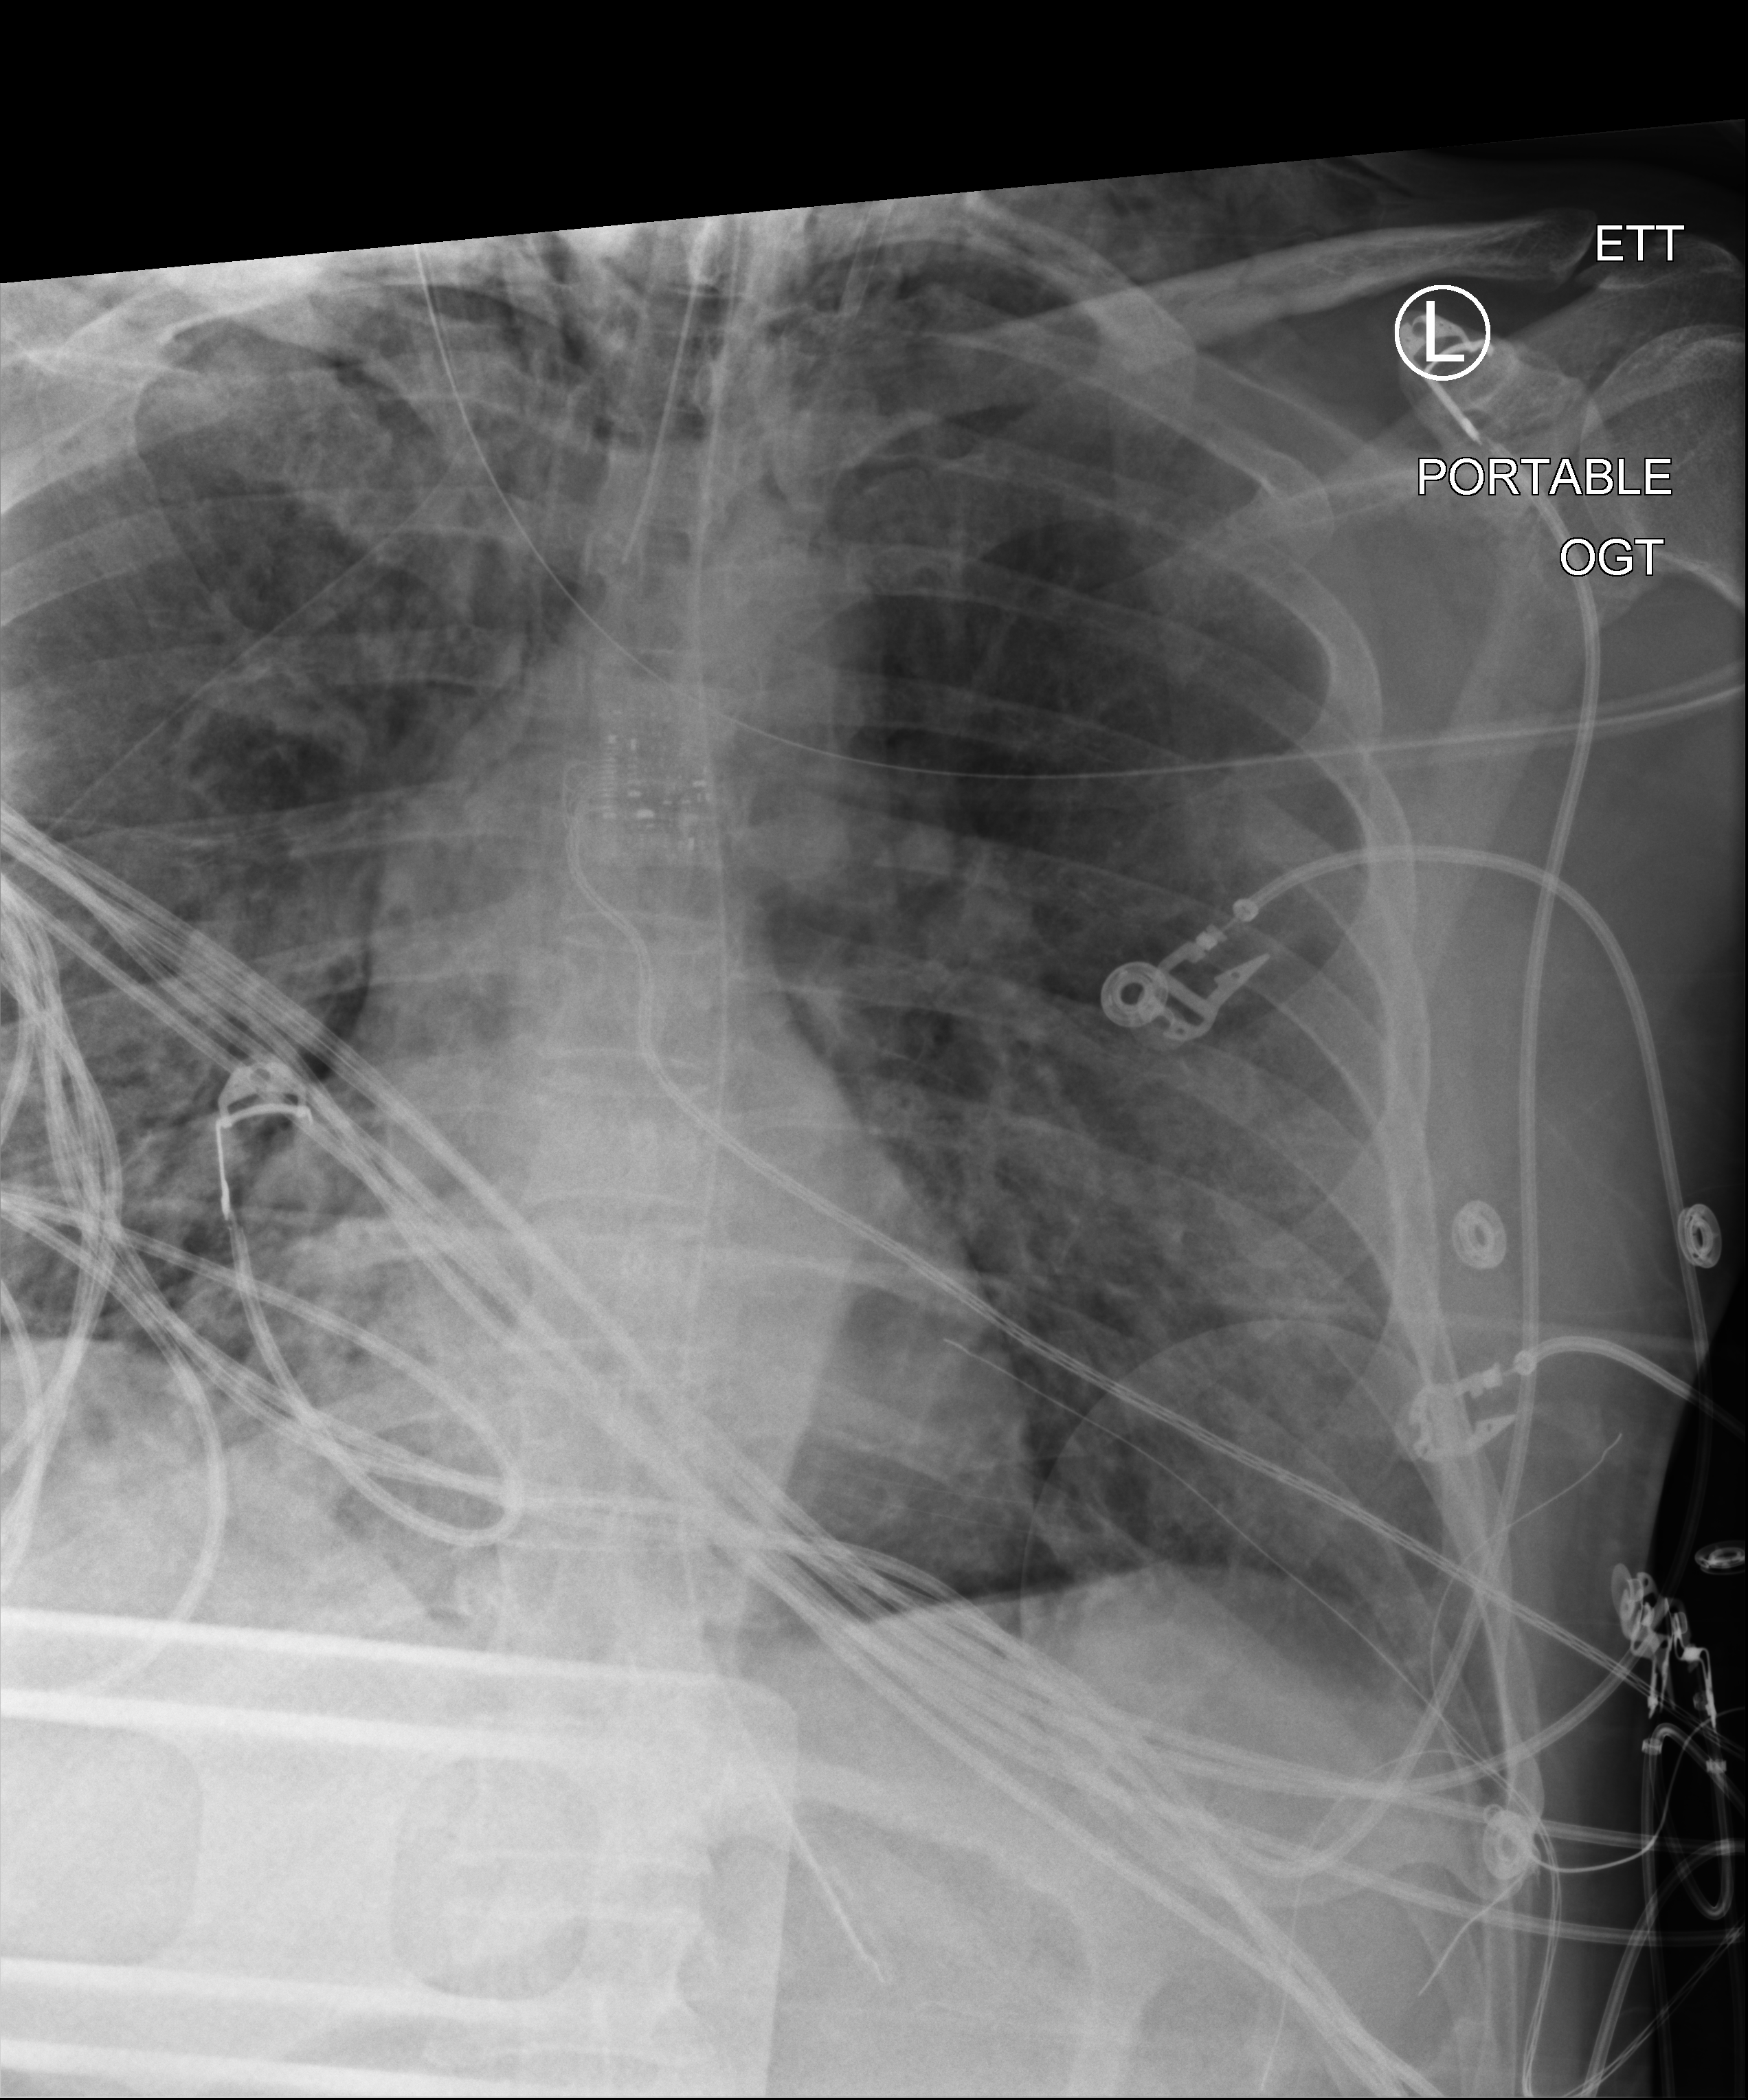
Chest X-ray (portable), anteroposterior (AP) projection. Male patient hospitalised with COVID-19, age 60–74 years.
Admission-level facts for this patient (not findings on this image; timing relative to this image not recorded):
- COPD (admission record): no
- mechanically ventilated during this hospital stay: yes